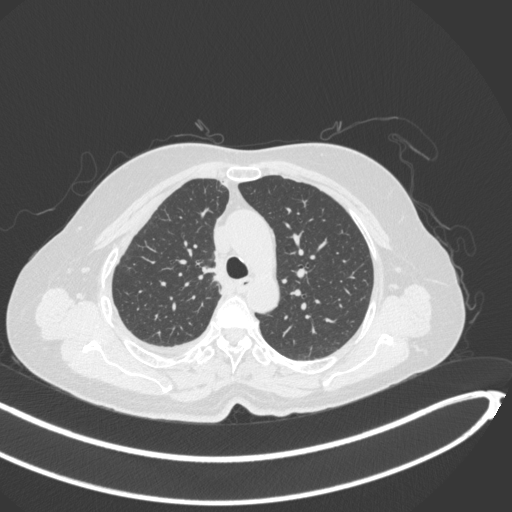
Chest CT, one axial slice. Position 216 of 297 along the scan axis. 120 kVp. Lung window (W 1500 / L -600 HU). 1 mm slice thickness. 512 × 512 image matrix. Patient: female, 64 years. From the clinical record (not read from this slice): clinical TNM (as recorded): T1b N0 M1.
Structures marked on this image (rectangle marked by the reading radiologist):
- lung tumour (recorded histology: adenocarcinoma): bounding box [x1, y1, x2, y2] px = [195, 259, 221, 286]